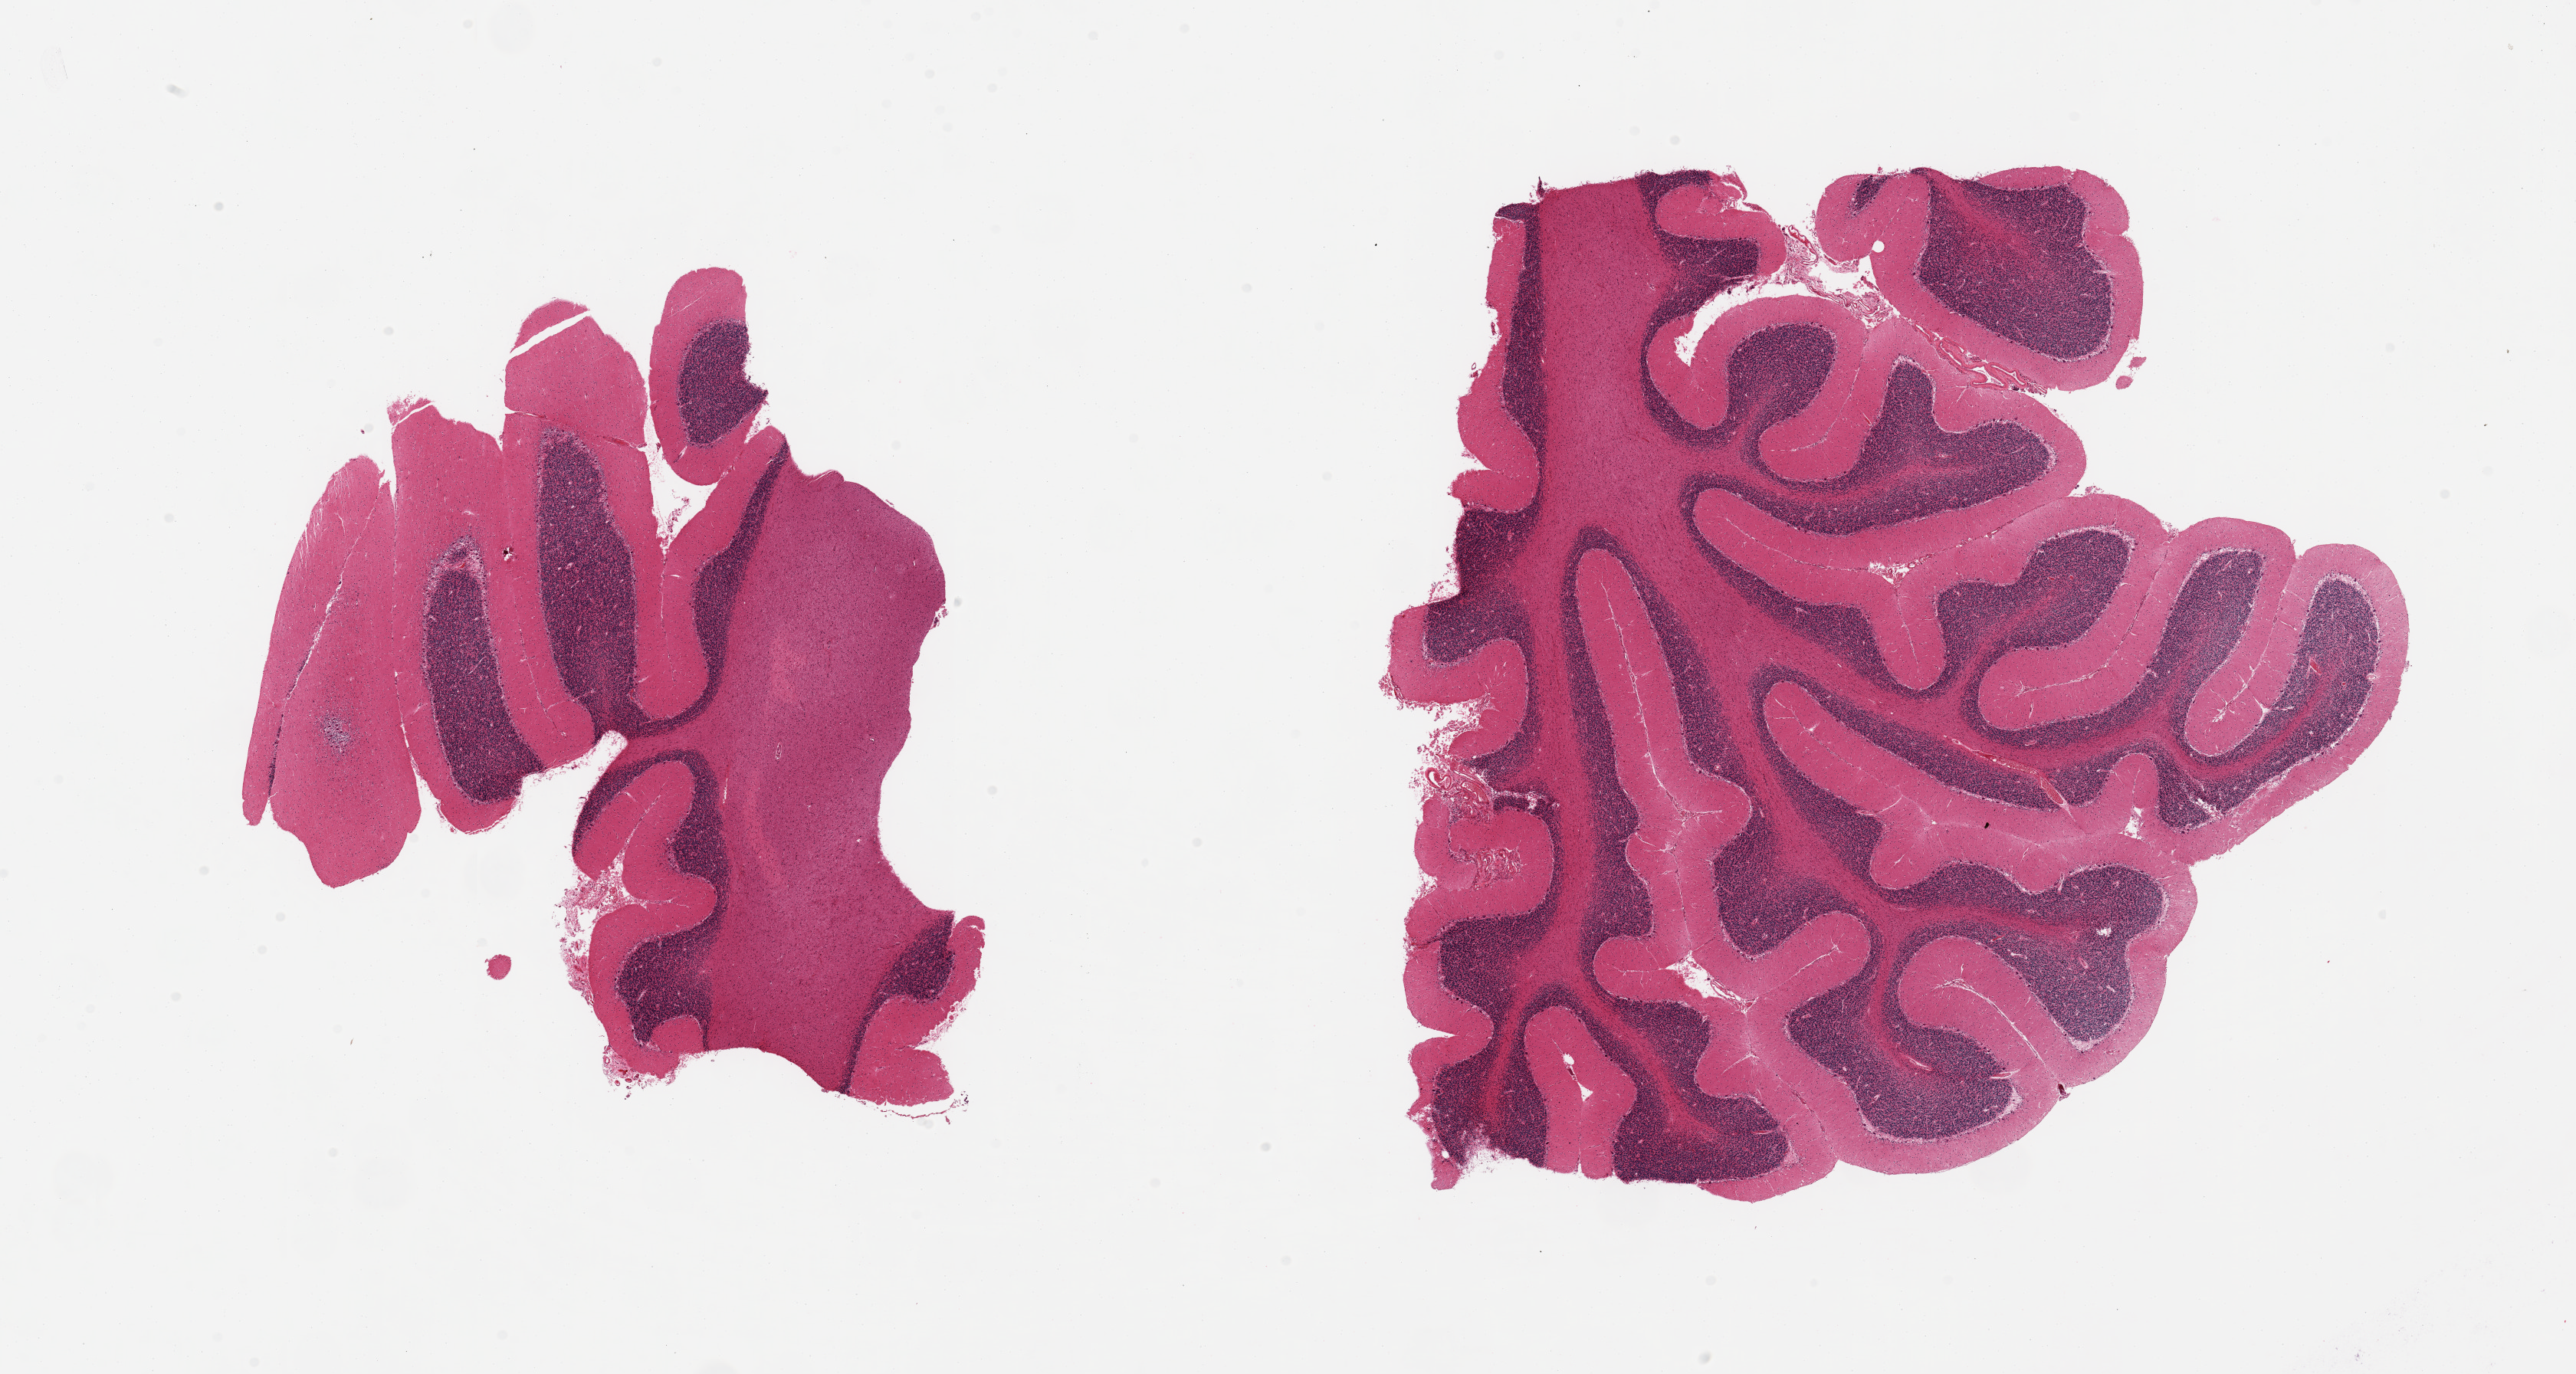
Digitized hematoxylin and eosin (H&E)-stained section, a low-resolution overview of the entire scanned area, about 26.6 x 14.2 mm, PAXgene-fixed, paraffin-embedded tissue, target tissue: cerebellum, tissue donor sample. Donor: male.
Review note (as recorded): 2 pieces; Purkinje cells well visualized.